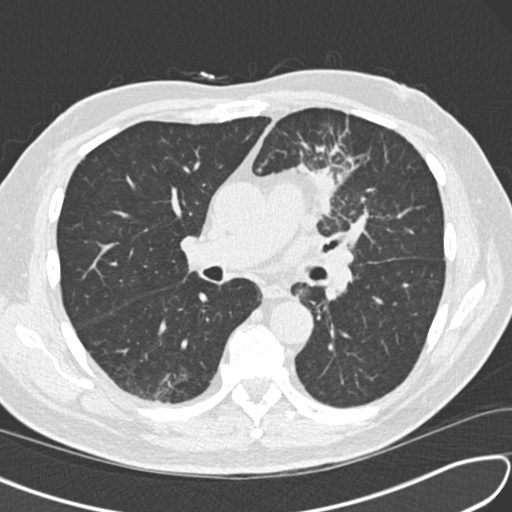
Low-dose screening chest CT, one axial slice; position 86 of 156 along the scan axis; lung window (W 1500 / L -600 HU); 2 mm slice thickness; 512 × 512 image matrix.
Outlined on this slice (outlined manually by an expert reader):
- lesion 1 (tumor, upper lobe of left lung): bounding box [x1, y1, x2, y2] px = [299, 164, 334, 217]